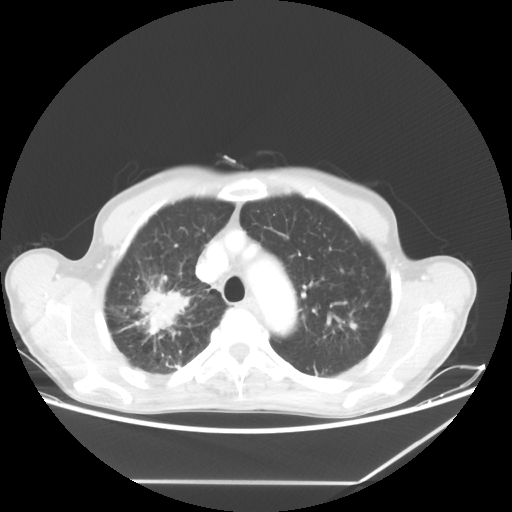
Chest CT, one axial slice; slice 49 of 65 in the series (ordered by position); 80 kVp; lung window (W 1500 / L -600 HU); 5 mm slice thickness; 512 × 512 image matrix, field of view 397 × 397 mm. Male patient, age 68 years. From the clinical record (not read from this slice): clinical TNM (as recorded): T3 N3 M0.
Structures marked on this image (bounding box drawn by a radiologist):
- lung tumour (recorded histology: adenocarcinoma): bounding box <132,268,198,351> (left, top, right, bottom; pixels)